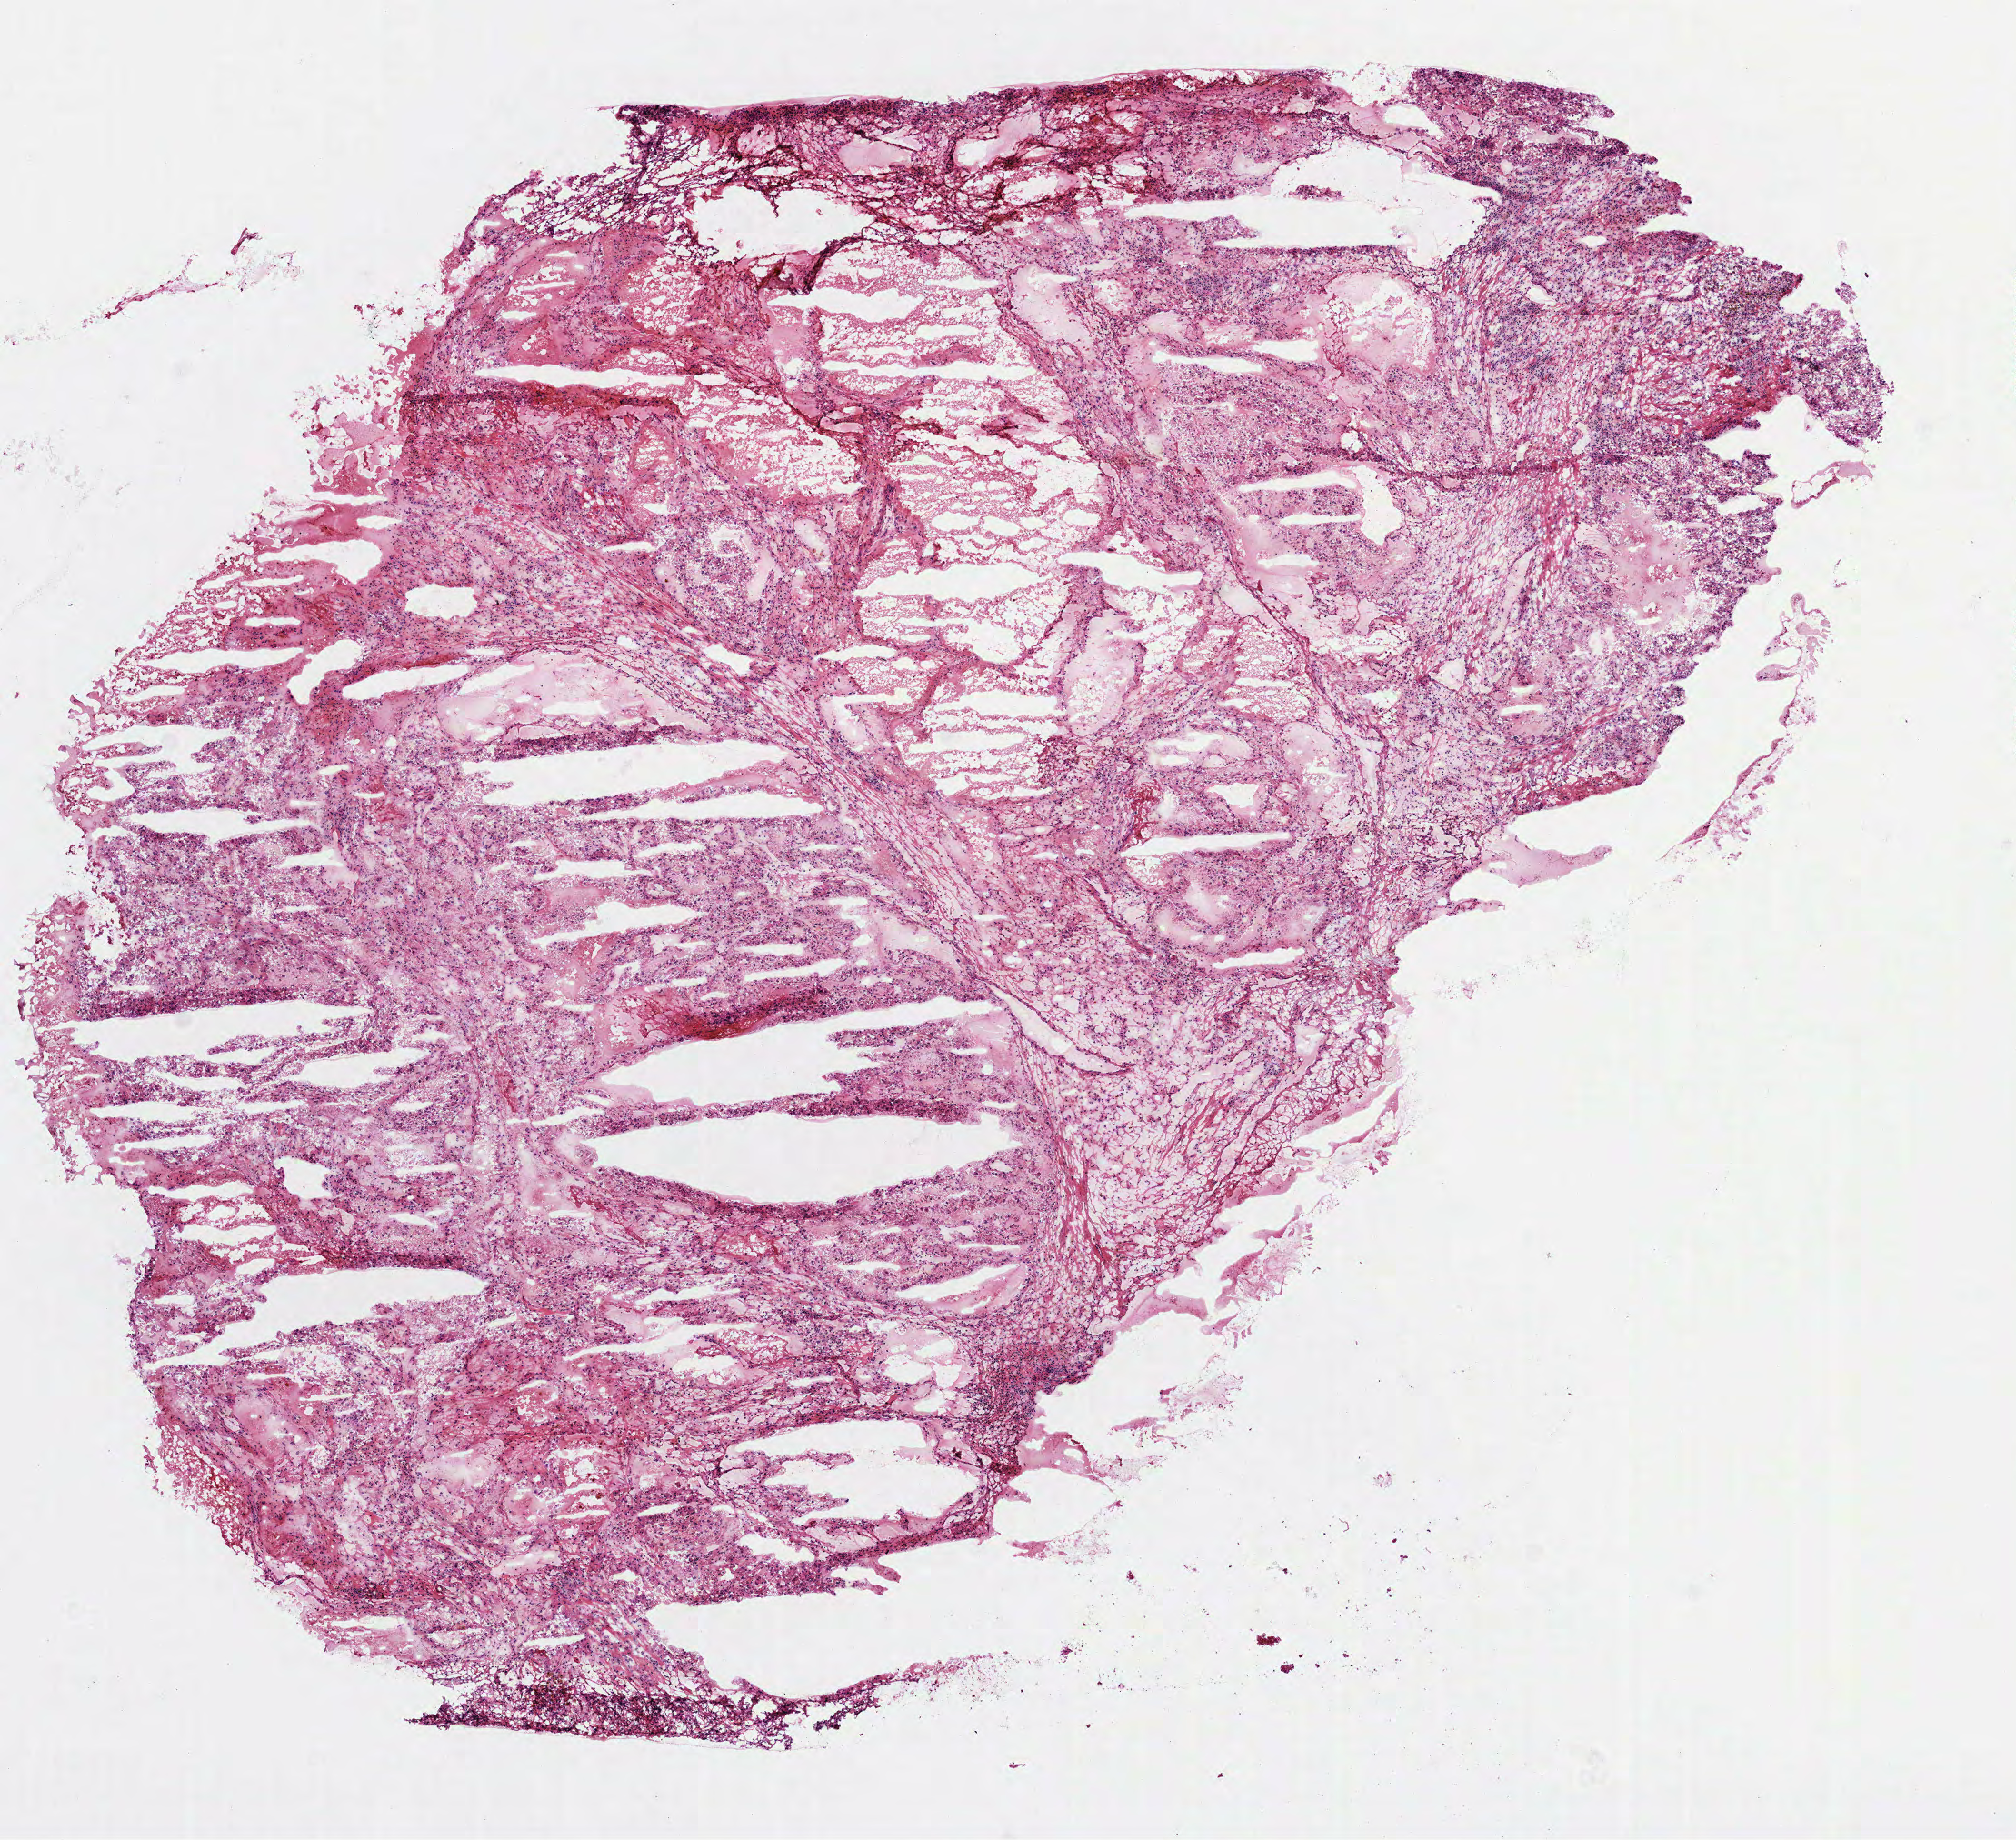
H&E whole-slide image, shown as a low-resolution overview of the whole scanned area (about 8.9 x 8.2 mm); frozen section from the top of the tissue portion; sample: primary tumour, kidney. Female patient; age at initial diagnosis 65 years. Histologic grade: G3 (poorly differentiated). Composition of this section per pathologist review: tumour cells 95%, tumour nuclei 80%, normal cells 0%, stromal cells 0%, necrosis 5%. Inflammatory infiltration, as recorded: lymphocyte infiltration 2%, monocyte infiltration 4%, neutrophil infiltration 0%.
• AJCC pathologic stage: I
• diagnosis: Clear cell adenocarcinoma, NOS
• TNM: T1a NX MX
• laterality: left